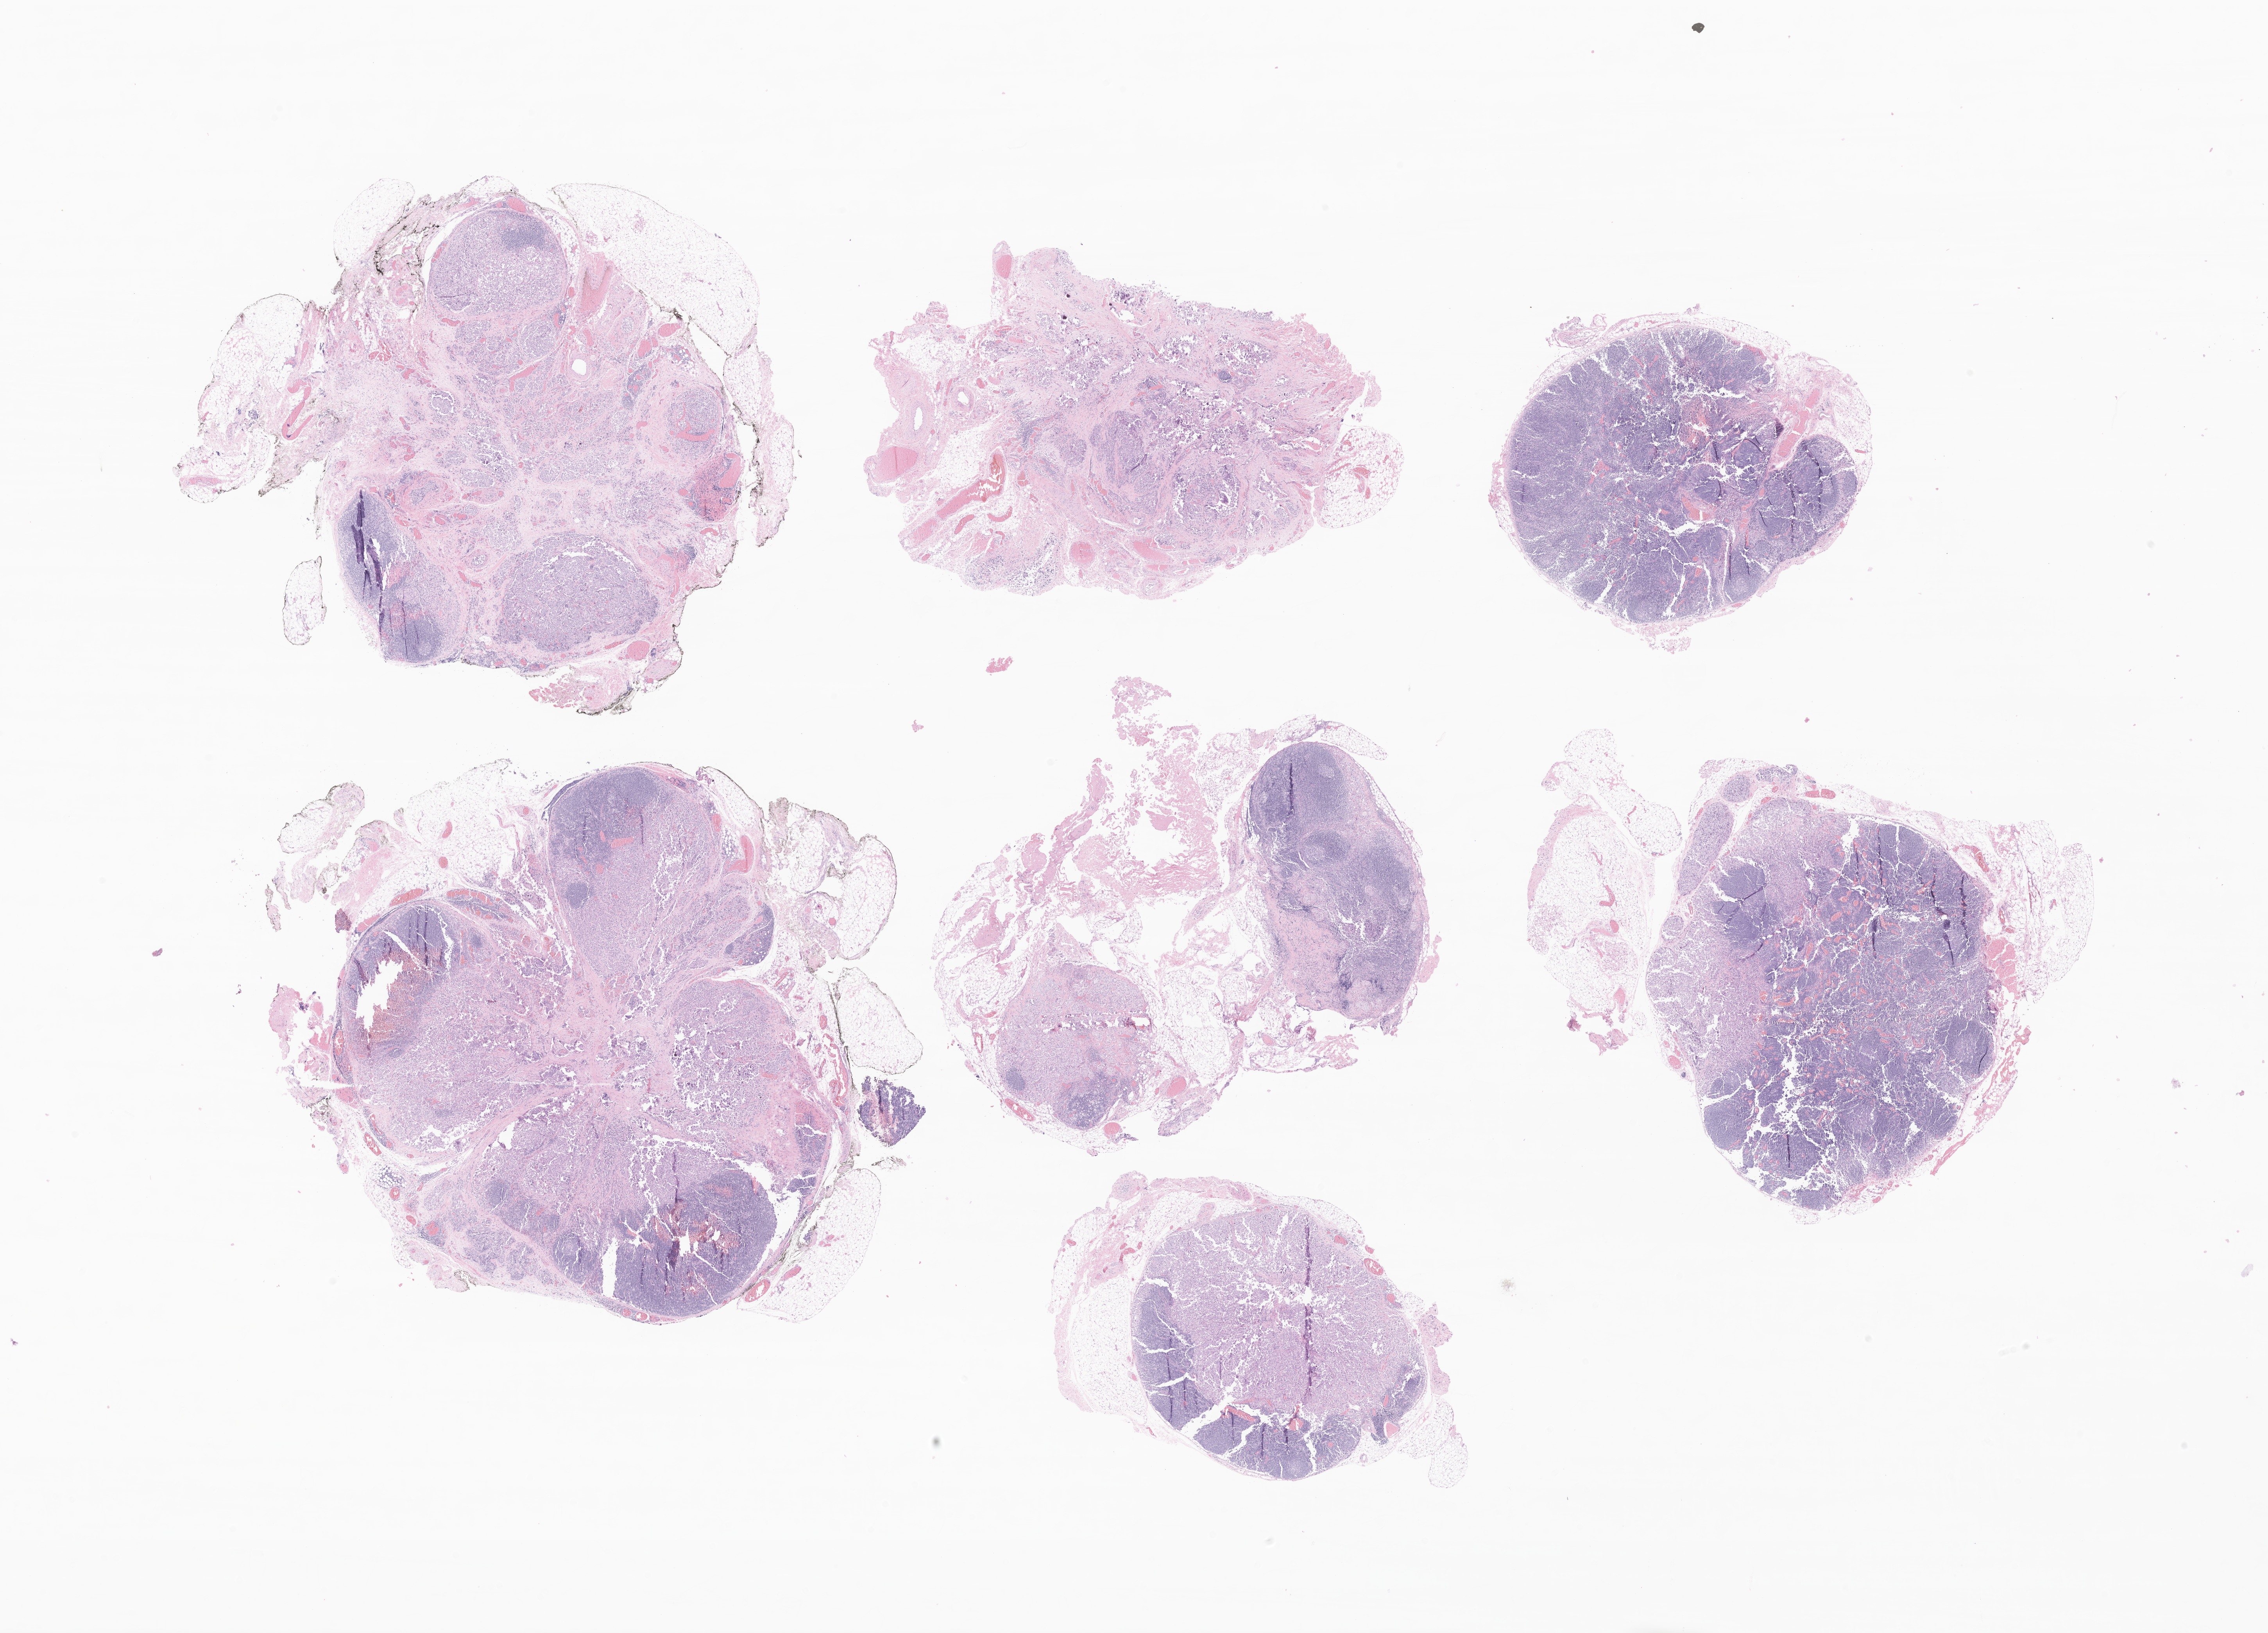
Haematoxylin and eosin whole-slide image of tumor tissue from the thyroid, shown as a low-resolution overview of the whole scanned area (about 24.5 x 17.6 mm); FFPE section. Patient: female, age 146 months (12 years 2 months).
Diagnosis (ICD-O-3 morphology term): Medullary carcinoma, NOS.